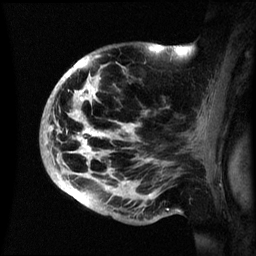
Breast MRI (dynamic contrast-enhanced), one sagittal slice. Position 40 of 60 along the scan axis. Dynamic contrast-enhanced series, image 2 of 3 at this slice position (ordered by acquisition). 1.5 T. TE 4.2 ms, TR 8.4 ms. 2.4 mm slice thickness. 256 × 256 image matrix, field of view 230 × 230 mm. Female patient, age 48 years.
Annotated regions visible in this slice (semi-automatically segmented with operator editing):
- analysis volume of interest (the breast-tissue region the enhancement analysis was run in; not a lesion): bounding box [x1, y1, x2, y2] px = [42, 44, 195, 222]
- tumour enhancement mask (voxels above the 70 % enhancement threshold inside the analysis volume of interest): [46, 46, 154, 194]